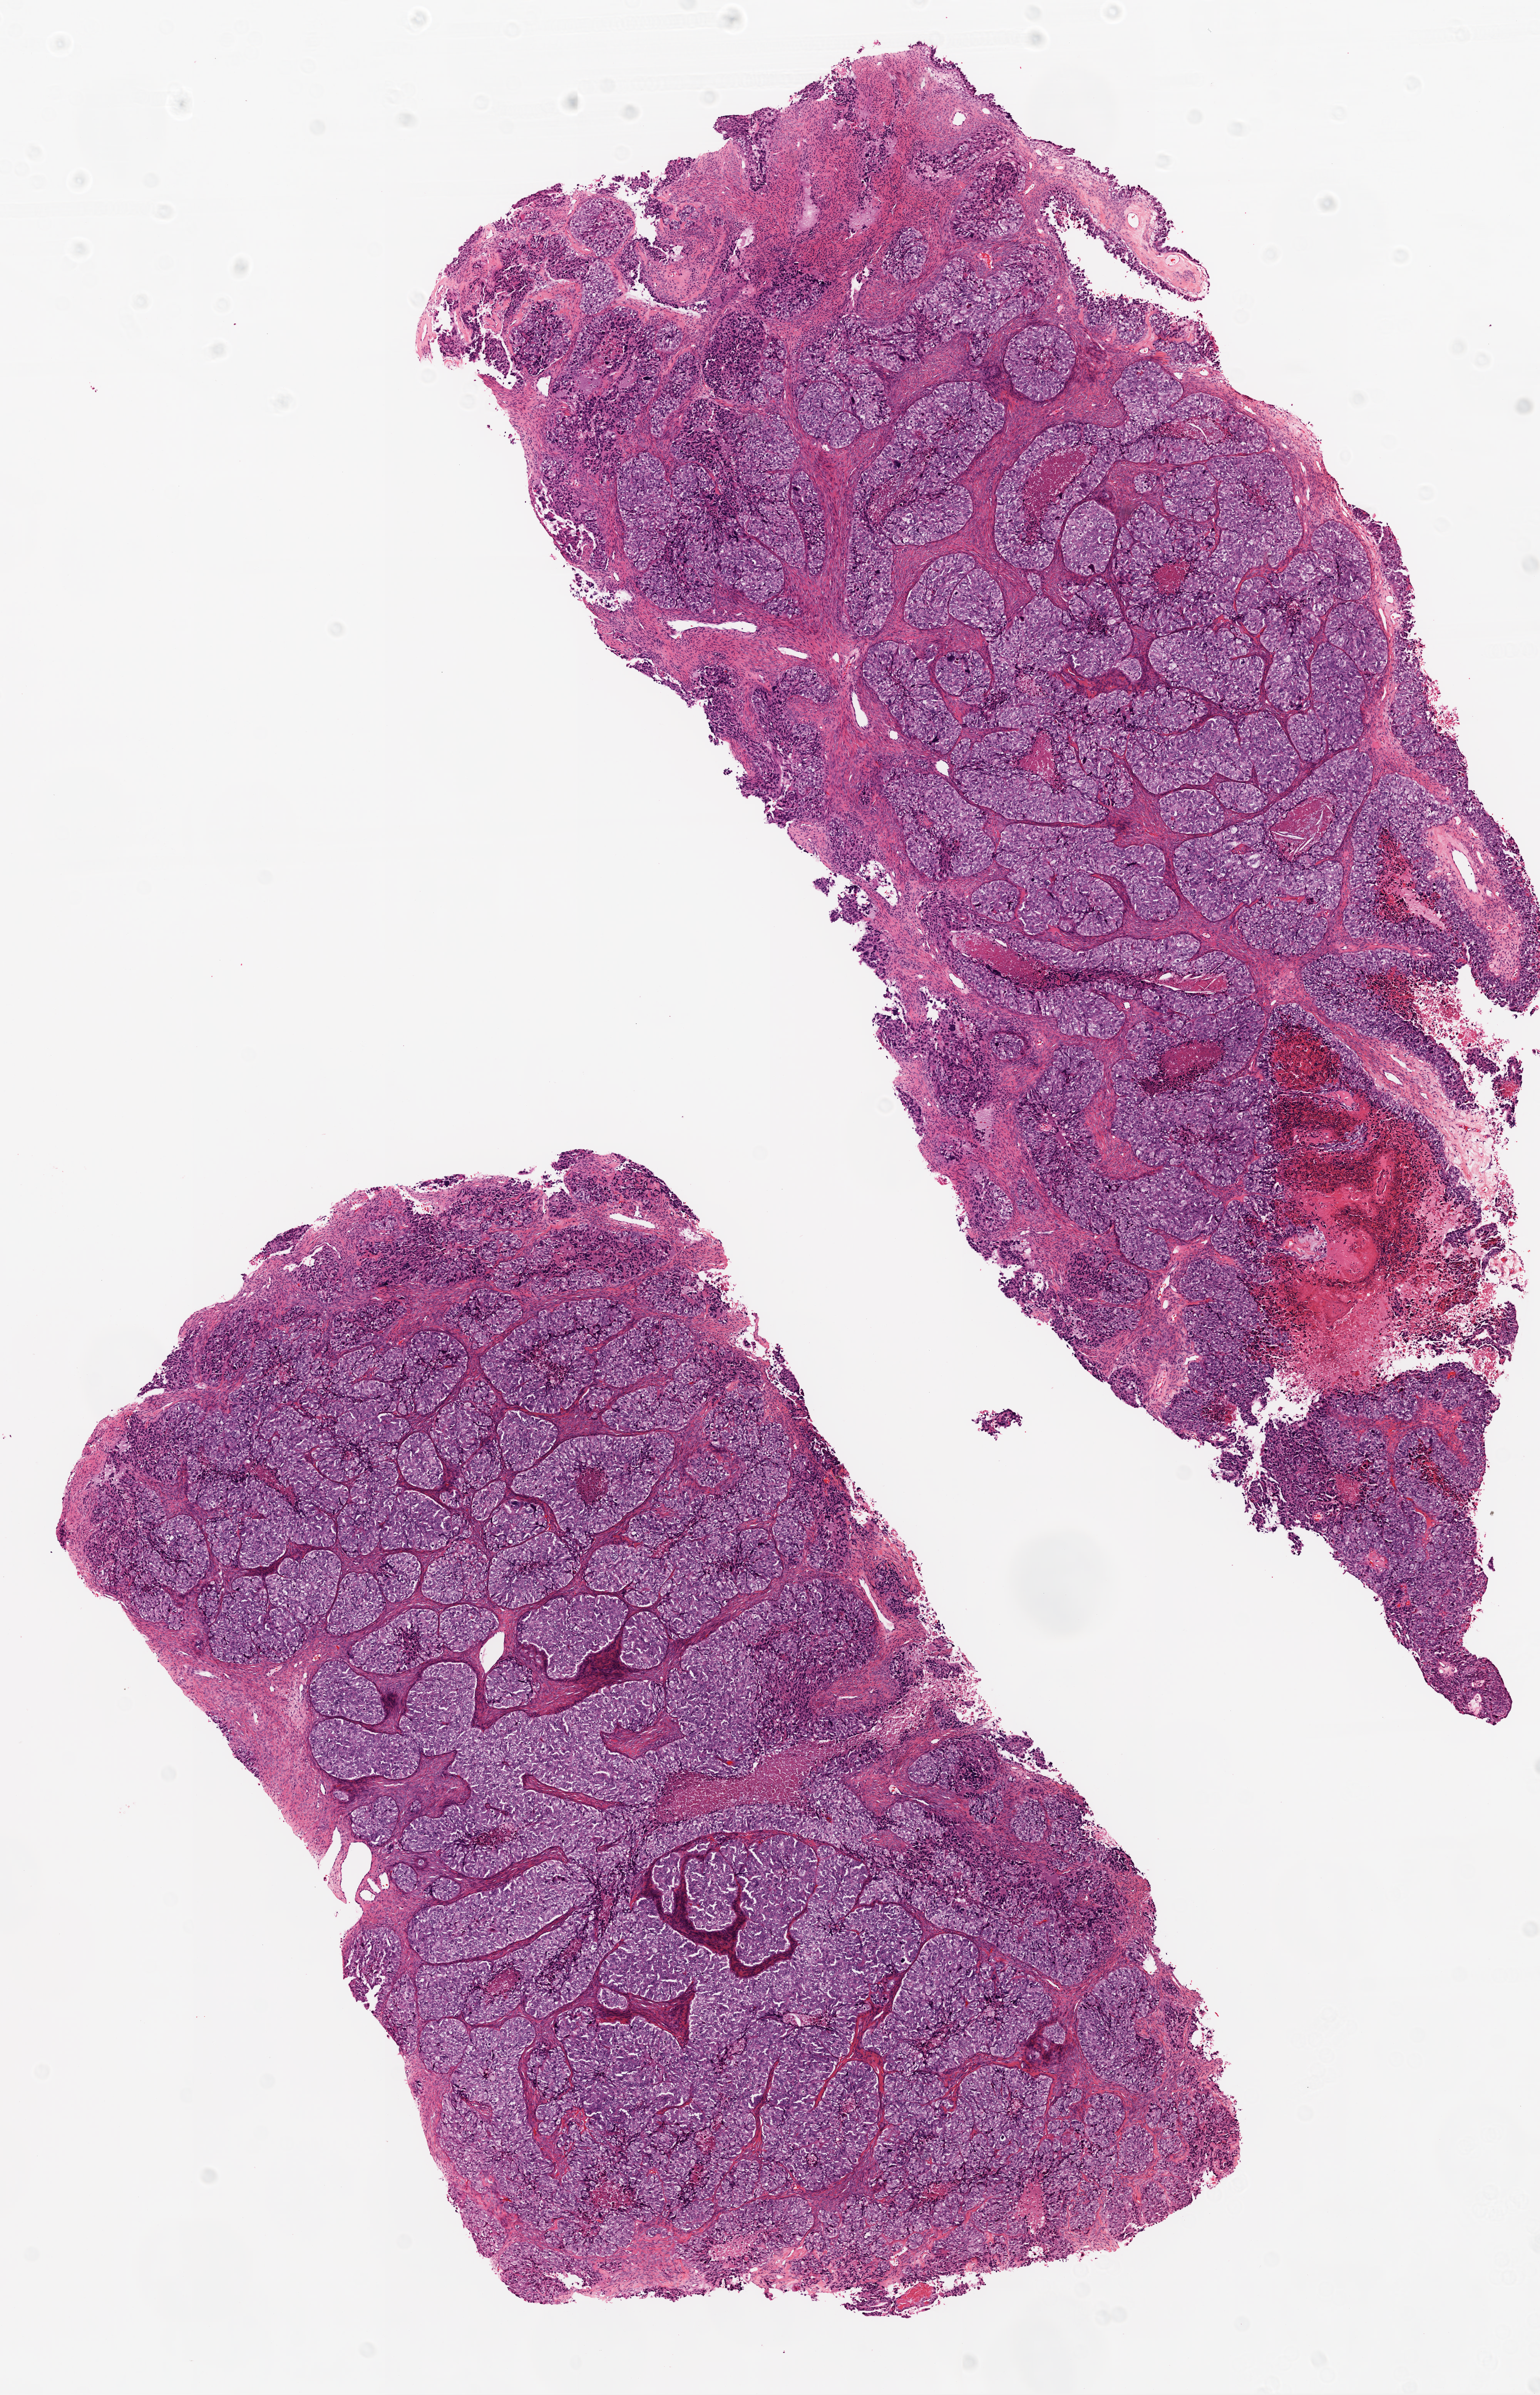
Whole-slide histology image, Hematoxylin and eosin (H&E) stained, low-resolution overview of the scanned area, about 8.0 x 12.5 mm (acquisition: 20x scan). Frozen section from the top of the tissue portion. Ovary, primary tumour sample. Patient: female, age at initial diagnosis 63 years. Histologic grade: G3 (poorly differentiated). Composition of this section per pathologist review: tumour cells 70%, tumour nuclei 80%, normal cells 0%, stromal cells 20%, necrosis 10%.
Pathologic diagnosis: Serous cystadenocarcinoma, NOS. FIGO stage: IIC.